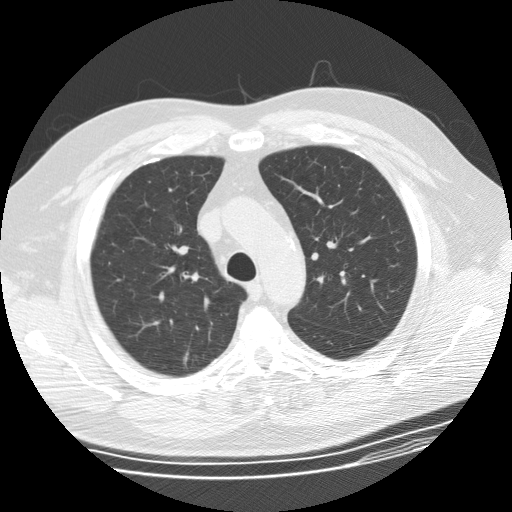
Low-dose screening chest CT, one axial slice. Slice 113 of 155 in the series (ordered by position). Reconstruction kernel STANDARD. 120 kVp. Lung window (W 1500 / L -600 HU). 2.5 mm slice thickness. 512 × 512 image matrix.
Outlined on this slice (outlined manually by an expert reader):
- lesion 1 (tumor, upper lobe of right lung): bounding box (x1, y1, x2, y2) in pixels: (183, 355, 188, 368)